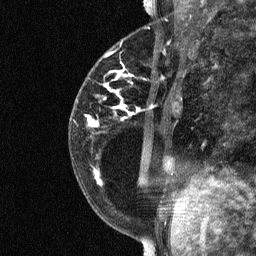
Breast MRI (dynamic contrast-enhanced), one sagittal slice; position 23 of 64 along the scan axis; dynamic contrast-enhanced study with each time point stored as its own series, time point 2 of 3 at this slice position (early post-contrast, ordered by acquisition time); 1.5 T; TE 4.8 ms, TR 27 ms; 2 mm slice thickness; 256 × 256 image matrix, field of view 180 × 180 mm. Patient: female, 34 years. From the clinical record (not read from this slice): setting: breast cancer imaged before/during neoadjuvant chemotherapy; receptor status: HR-positive, HER2-negative.
Outlined on this slice (semi-automatically segmented with operator editing):
- analysis volume of interest (the breast-tissue region the enhancement analysis was run in; not a lesion): box from (x=78, y=44) to (x=181, y=191) px
- tumour enhancement mask (voxels above the 90 % enhancement threshold inside the analysis volume of interest): (x=88, y=90)–(x=132, y=183)